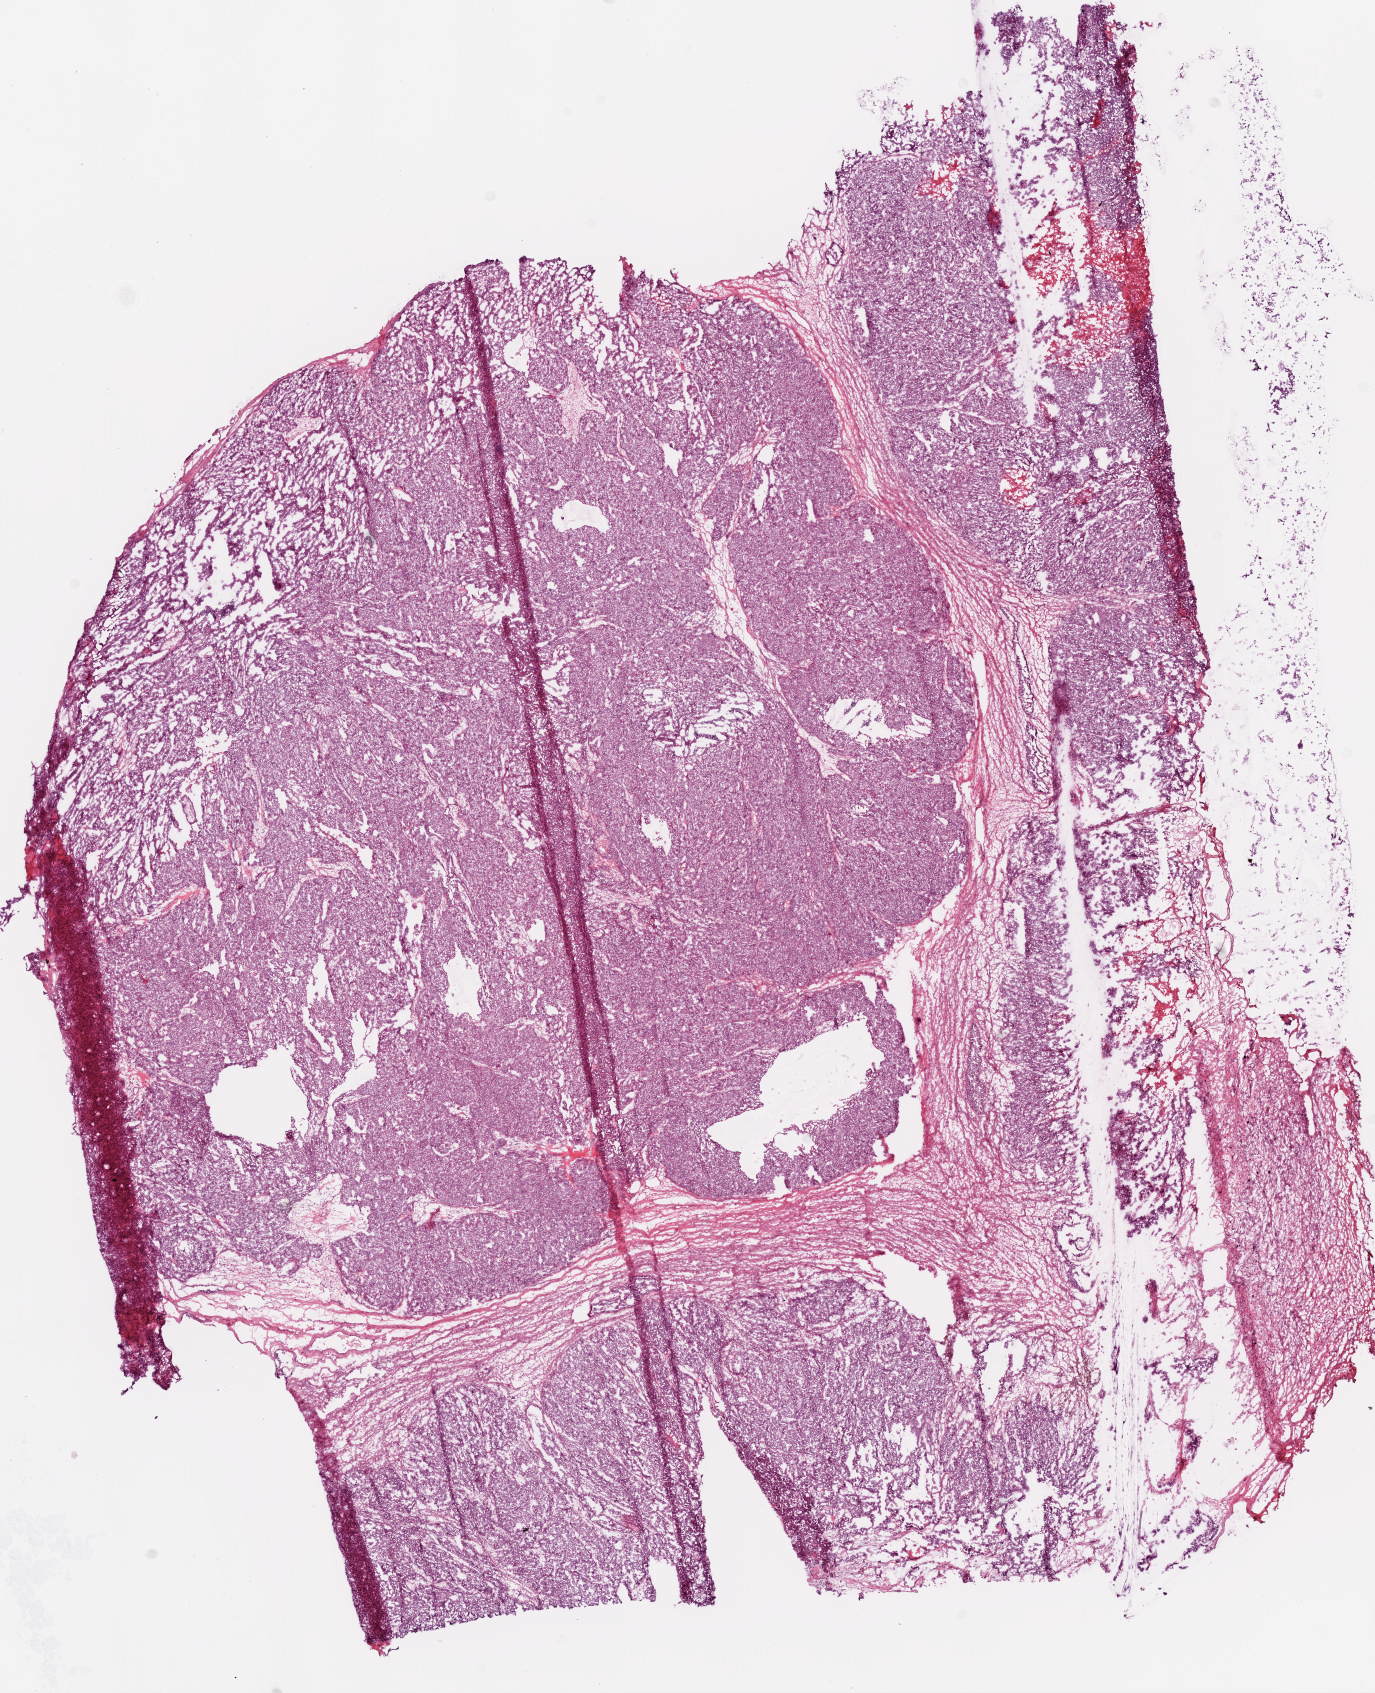
Whole-slide histology image, H&E — whole scanned area (about 11.0 x 13.6 mm, slide scanned at 20x) shown as a low-resolution overview, frozen section, ovary, primary tumour sample. Patient: female, age at initial diagnosis 66 years. Histologic grade: G3 (poorly differentiated). Pathologist review of this section (percent, as recorded): tumour cells 70%, tumour nuclei 93%, normal cells 25%, stromal cells 0%, necrosis 5%.
• diagnosis: Serous cystadenocarcinoma, NOS
• FIGO stage: IIIC